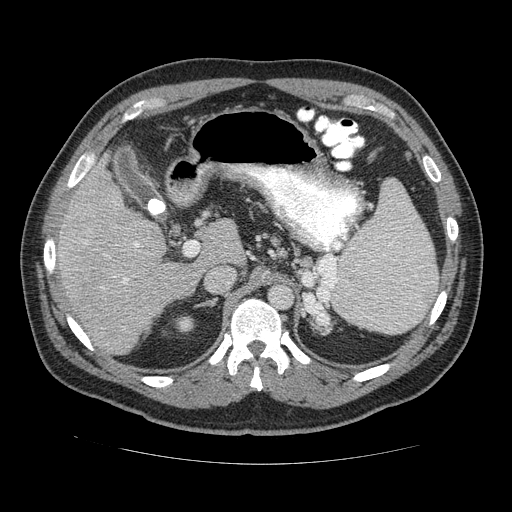
Contrast-enhanced abdominal CT (liver protocol), one axial slice; 120 kVp; soft-tissue window (W 400 / L 40 HU); 2.5 mm slice thickness; 512 × 512 image matrix, field of view 400 × 400 mm. Case-level facts recorded for this patient, not image findings: diagnosis: hepatocellular carcinoma (patient treated with transarterial chemoembolisation; whether this scan precedes or follows treatment is not stated here); TNM stage (as recorded): Stage-II; Child-Pugh class: B; tumour differentiation: moderately differentiated; tumour size: 4.8 cm.
Structures marked on this image (semi-automatically segmented with operator editing):
- liver parenchyma outside the tumour (the mass and vessels are separate outlines, so this box may not span the whole liver): bounding box (x1, y1, x2, y2) in pixels: (50, 160, 209, 354)
- liver vessels: (51, 231, 141, 289)